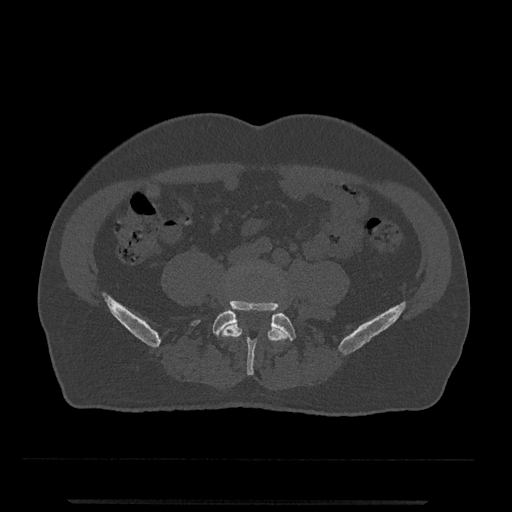
CT including the spine, one axial slice. Reconstruction kernel Br40s/3. 120 kVp. Bone window (W 1800 / L 400 HU). 512 × 512 image matrix. Patient: male, 63 years. From the clinical record (not read from this slice): primary cancer: prostate.
Annotated regions visible in this slice (semi-automatic segmentation, software-assisted and operator-edited):
- L4 vertebra: box from (x=221, y=268) to (x=289, y=367) px
- L5 vertebra: (x=191, y=301)–(x=317, y=375)